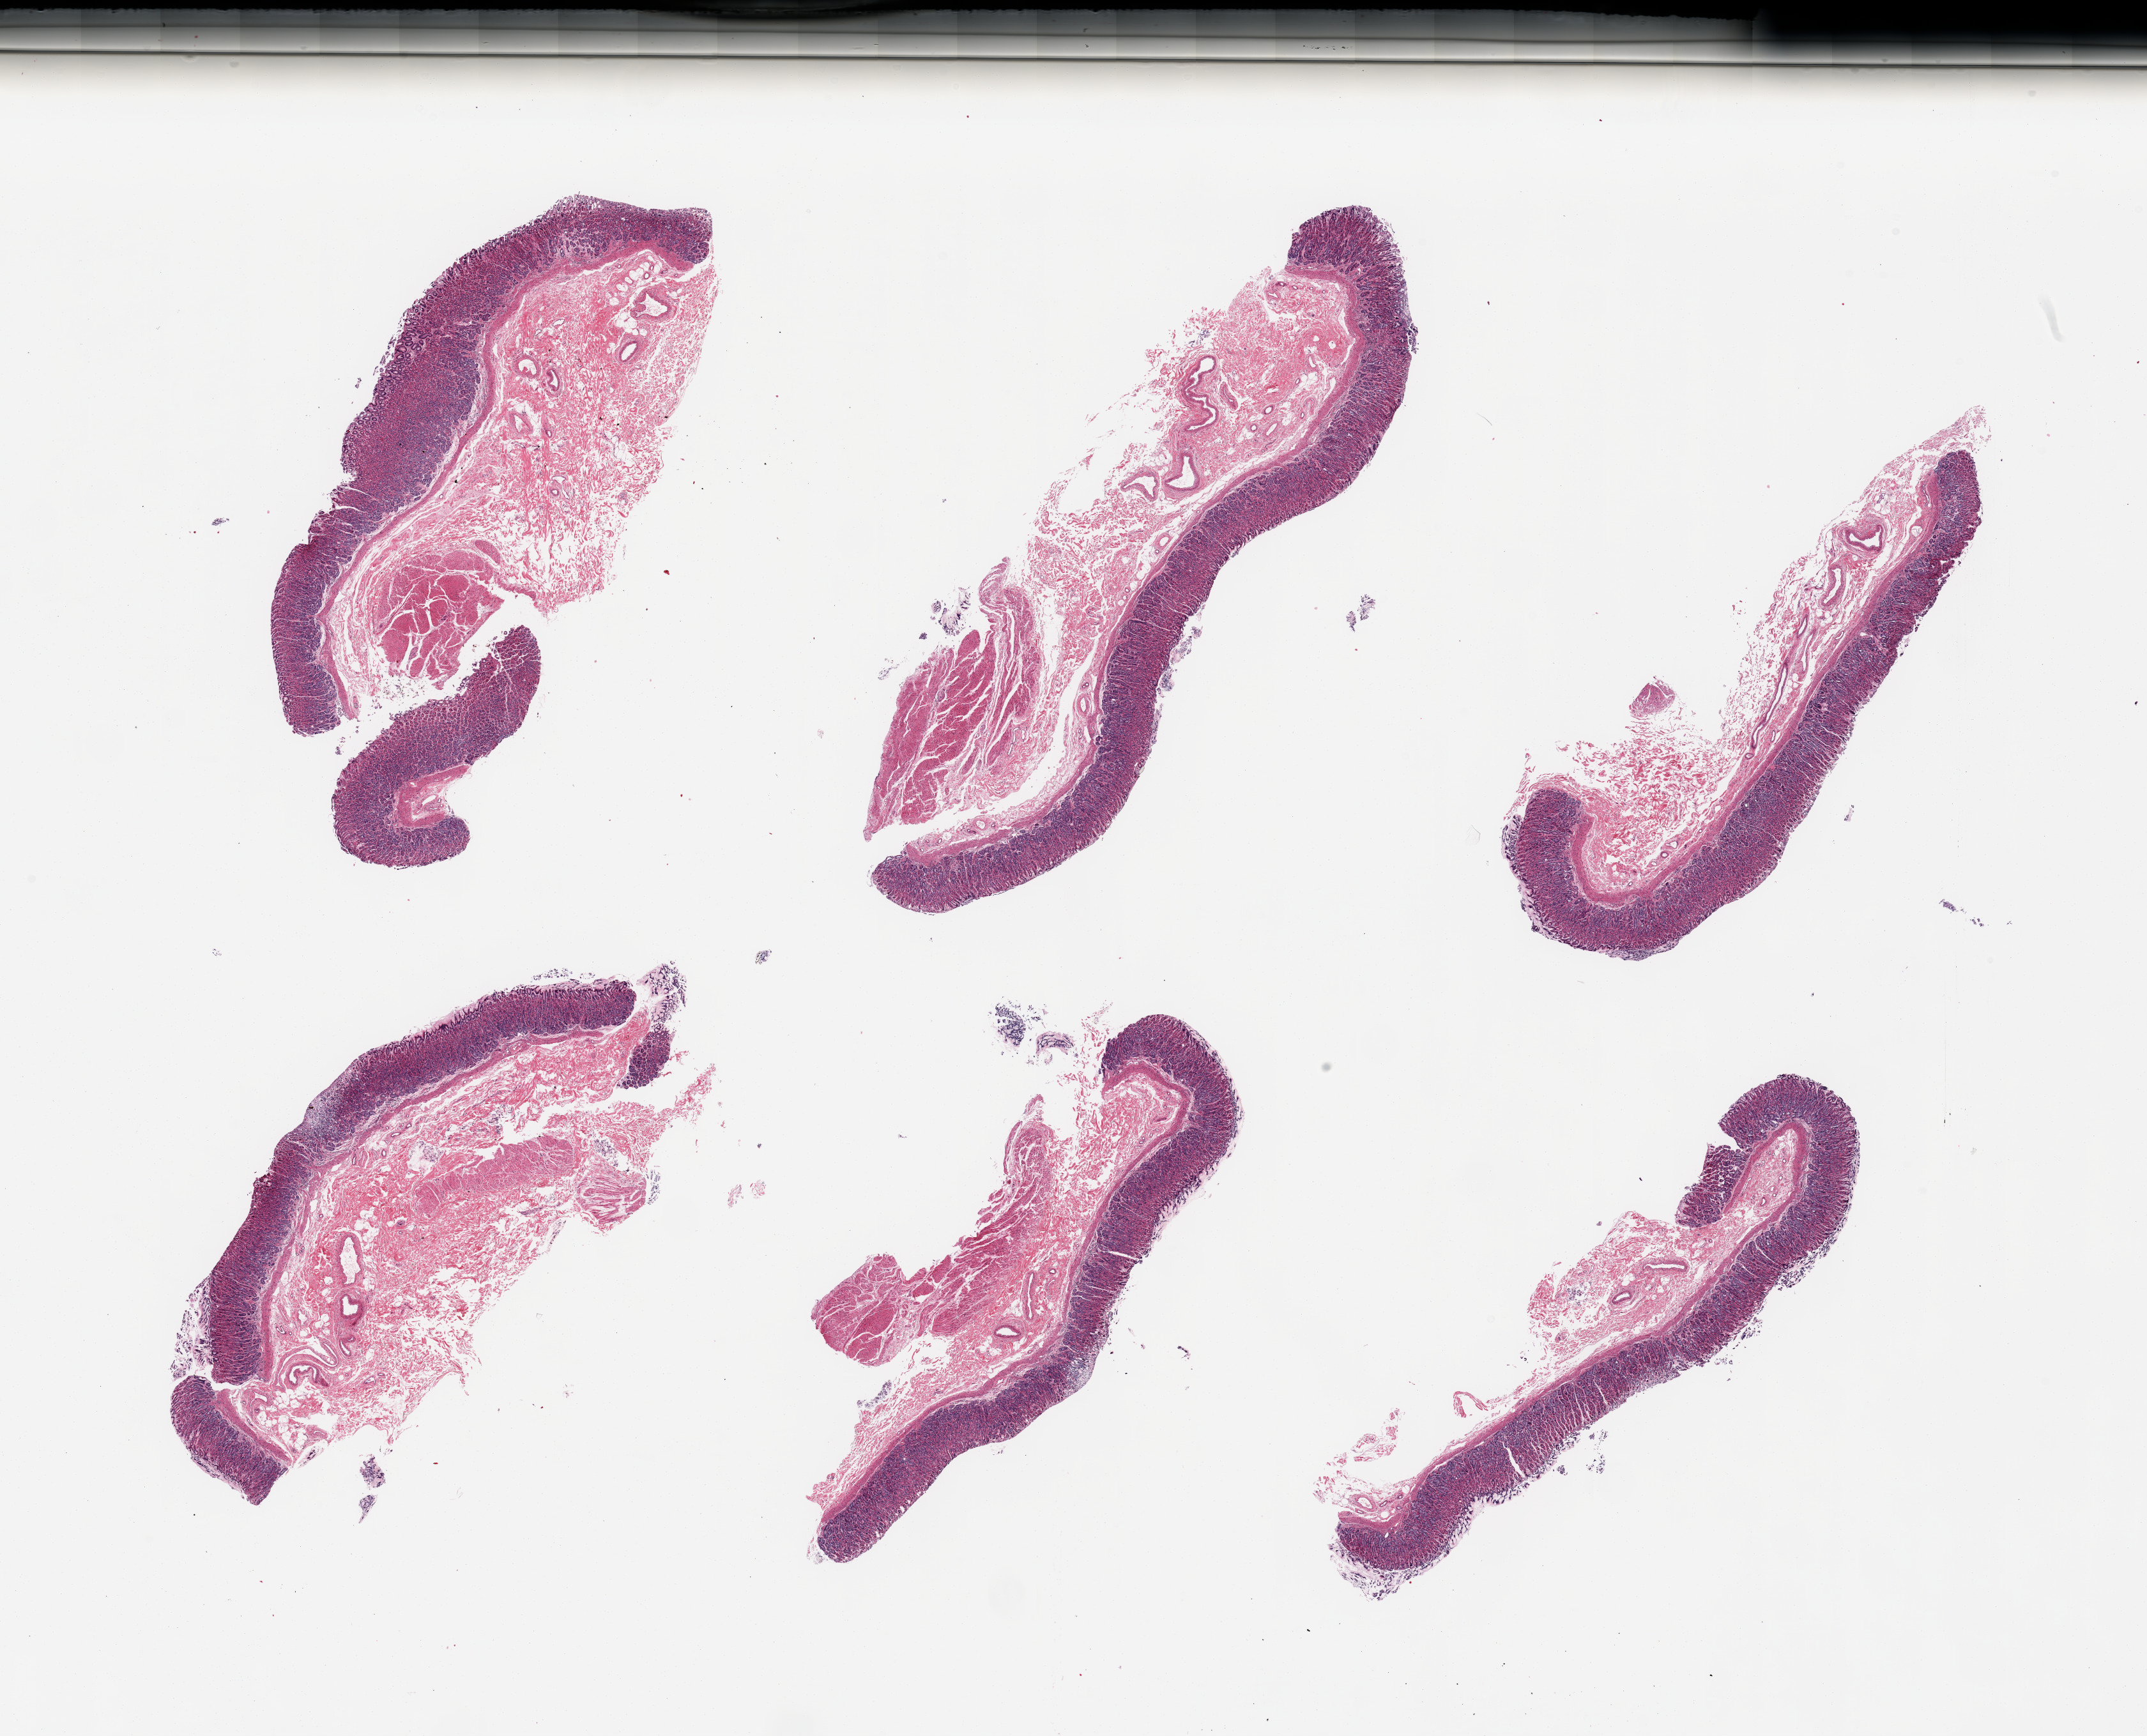
Haematoxylin and eosin whole-slide image — low-resolution overview of the scanned area, about 26.6 x 21.5 mm (slide scanned at 20x). PAXgene-fixed paraffin-embedded (PFPE) section. Section of stomach (target tissue). Tissue donor sample. Donor: male.
Reviewer comment on this tissue sample: 6 pieces; little muscularis in 4 pieces, none in 2.